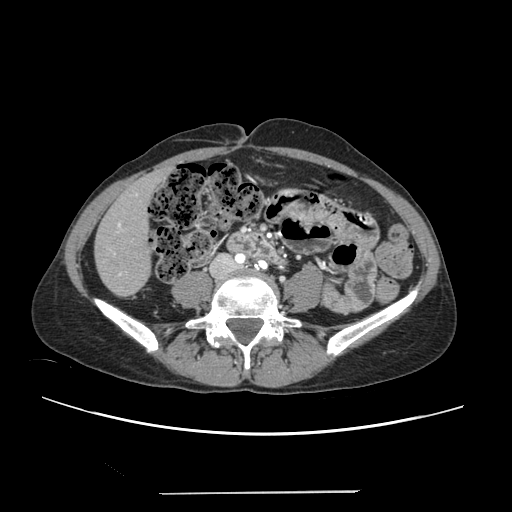
Contrast-enhanced abdominal CT, one axial slice. Position 42 of 240 along the scan axis. Intravenous contrast given. Soft-tissue window (W 400 / L 40 HU). 512 × 512 image matrix, field of view 371 × 371 mm. Female patient, age 60 years. From the clinical record (not read from this slice): diagnosis: colorectal cancer liver metastases, imaged before liver resection; multiple liver metastases: no; largest metastasis: 1.5 cm; disease in both lobes: no.
Outlined on this slice (expert manual segmentation):
- liver: bounding box <96,172,165,295> (left, top, right, bottom; pixels)
- planned liver remnant (the part of the liver to remain after resection): <96,172,165,295>
- portal vein (with intrahepatic branches): <110,194,137,274>